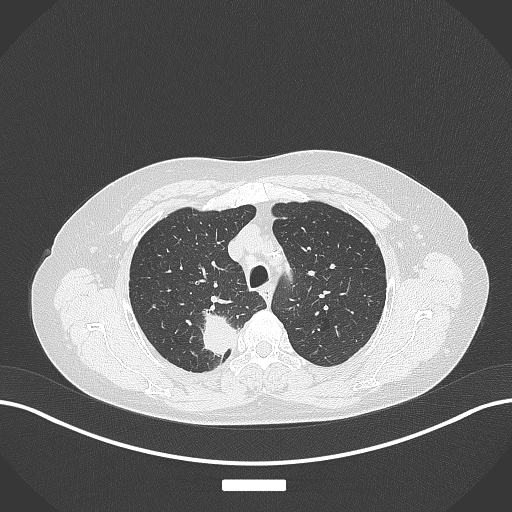
Chest CT, one axial slice; position 303 of 357 along the scan axis; reconstruction kernel B70f; lung window (W 1500 / L -600 HU); 1 mm slice thickness; 512 × 512 image matrix, field of view 400 × 400 mm. Patient: female, 62 years. Case-level facts recorded for this patient, not image findings: clinical TNM (as recorded): T1c N1 M0.
Annotated regions visible in this slice (bounding box drawn by a radiologist):
- lung tumour (recorded histology: squamous cell carcinoma): box from (x=198, y=307) to (x=240, y=362) px